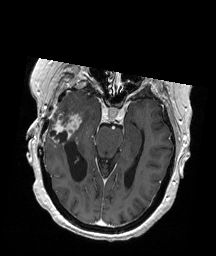
Brain MRI from a brain-tumour surgery series, one axial slice. Position 121 of 192 along the scan axis. T1-weighted post-contrast. 216 × 256 image matrix, field of view 211 × 250 mm. From the clinical record (not read from this slice): histopathology: Glioblastoma; WHO grade: 4; IDH mutation: no.
Outlined on this slice (manually delineated by an expert):
- tumour: bounding box <49,113,81,136> (left, top, right, bottom; pixels)